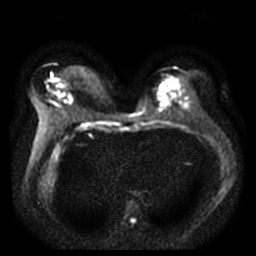
Breast MRI, one axial slice. Position 17 of 40 along the scan axis. Diffusion-weighted series; image 2 of 4 stored at this slice position (different b-values; order by instance number). 3 T. 256 × 256 image matrix. Female patient.
Structures marked on this image (expert manual segmentation):
- tumour on diffusion-weighted imaging: bounding box (x1, y1, x2, y2) in pixels: (51, 76, 58, 83)